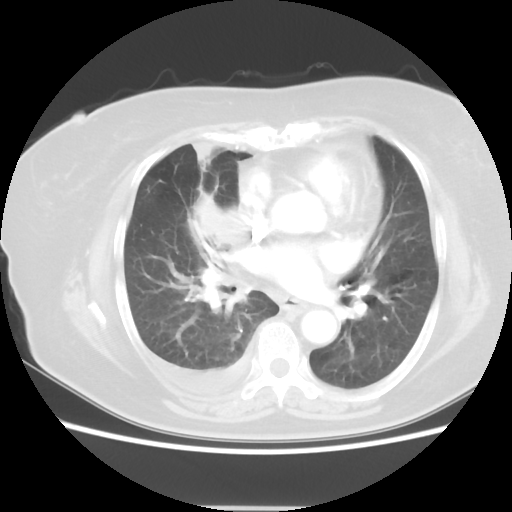
Chest CT, one axial slice. 120 kVp. Lung window (W 1500 / L -600 HU). 5 mm slice thickness. 512 × 512 image matrix. Female patient, age 73 years. Case-level facts recorded for this patient, not image findings: clinical TNM (as recorded): T3 N3 M1b; histopathological grade: G3.
Structures marked on this image (bounding box drawn by a radiologist):
- lung tumour (recorded histology: small cell carcinoma): bounding box (x1, y1, x2, y2) in pixels: (186, 186, 248, 256)